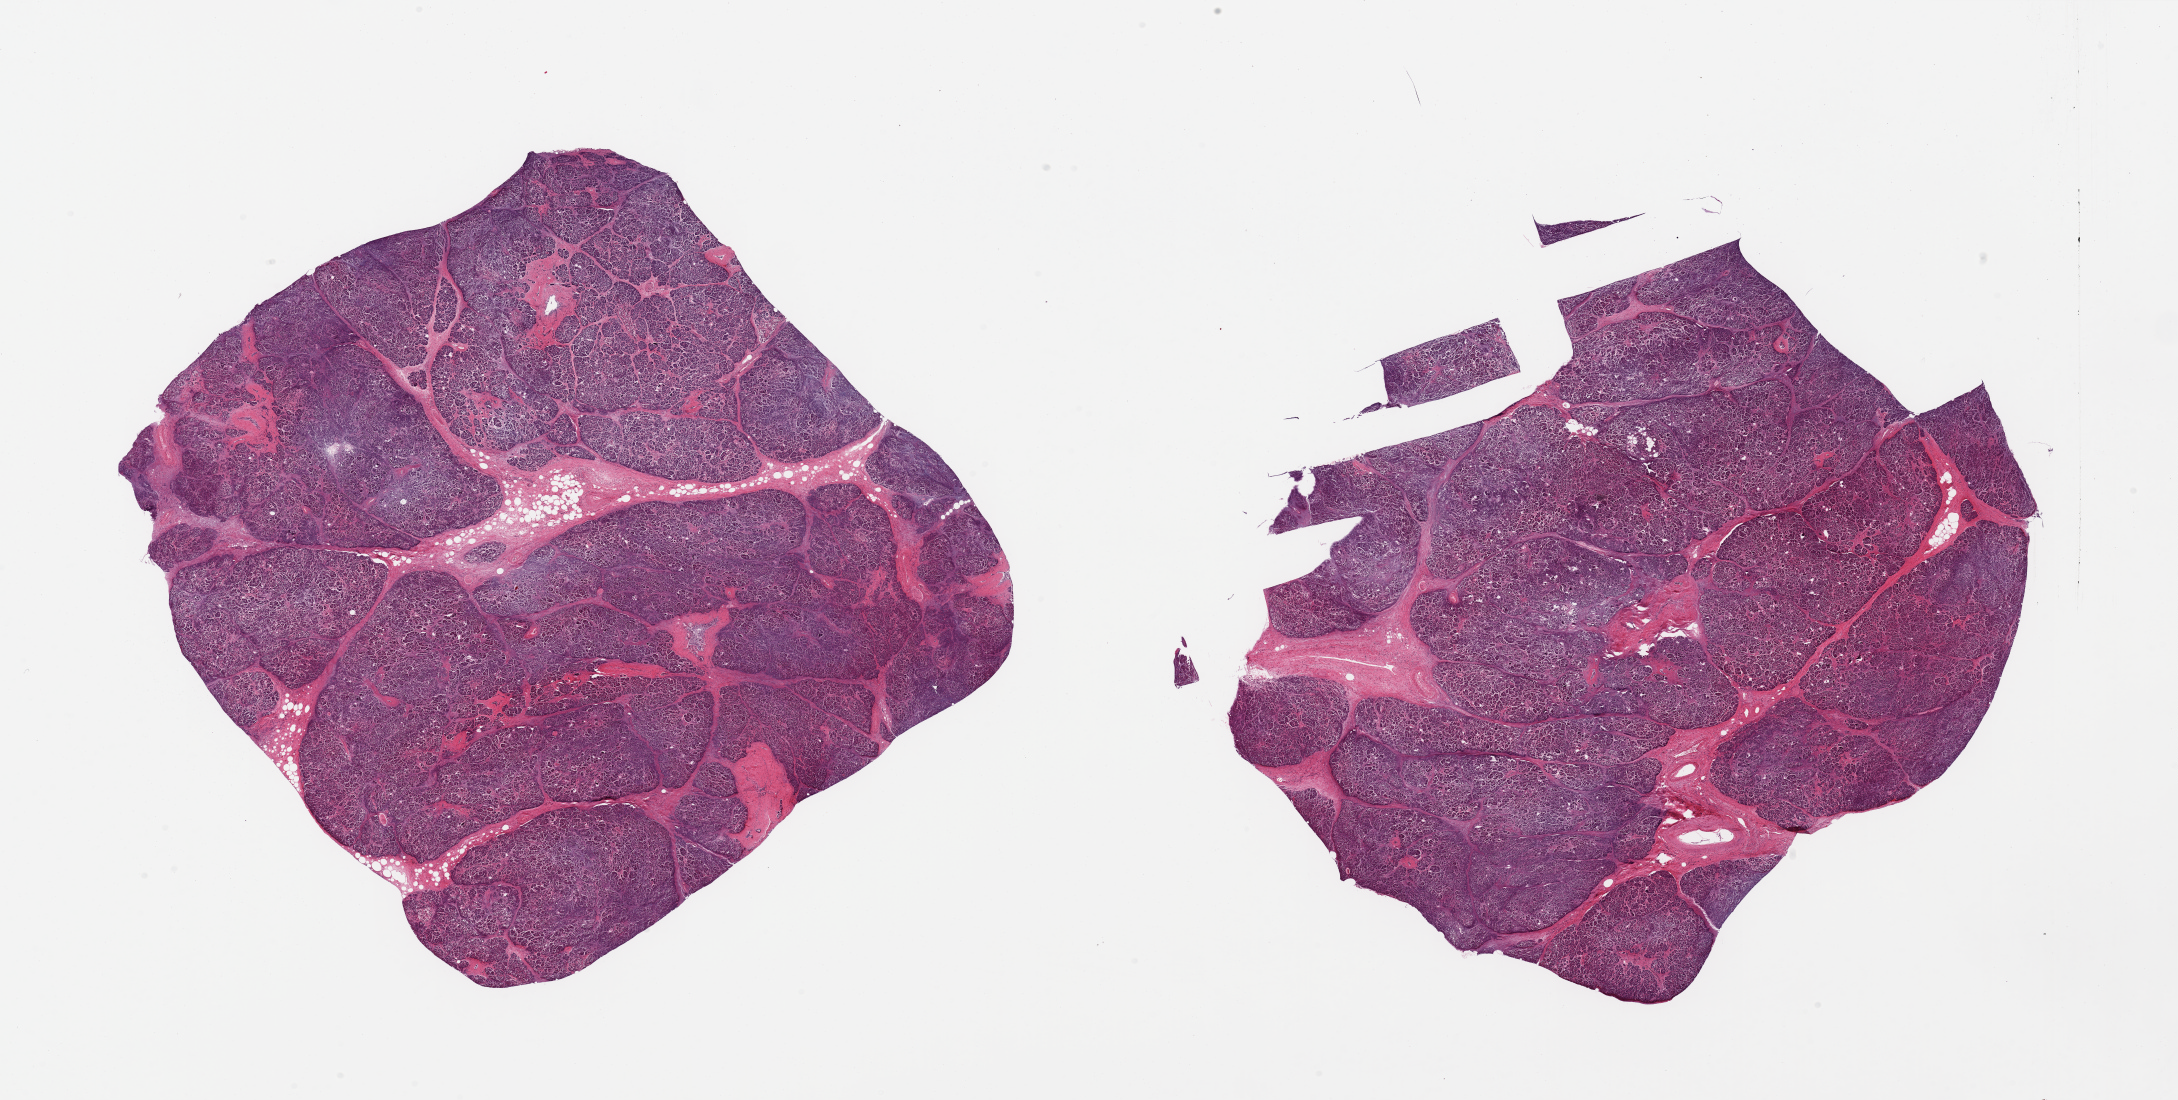
H&E whole-slide image — low-resolution overview of the scanned area, about 34.5 x 17.4 mm (acquisition: 20x scan); PAXgene-fixed paraffin-embedded (PFPE) section; sampled site (target tissue): pancreas; donor tissue sample. Male donor.
Review note (as recorded): 2 pieces, moderately-markedly advanced saponification. Islets not visible.